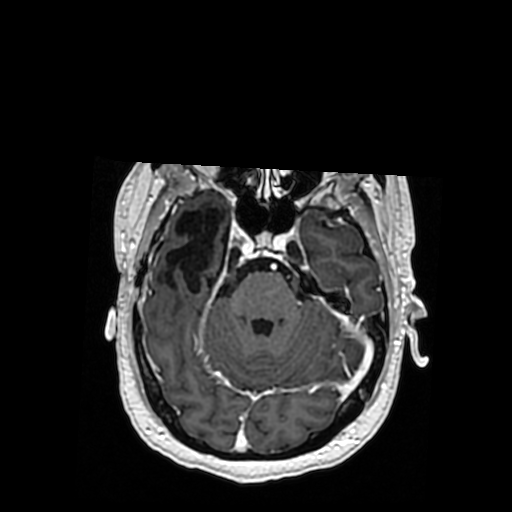
Brain MRI from a brain-tumour surgery series, one axial slice; T1-weighted post-contrast; 512 × 512 image matrix. Case-level facts recorded for this patient, not image findings: histopathology: Oligodendroglioma; WHO grade: 3; IDH mutation: yes; tumour location: Right Posterior Temporal Inferior Parietal.
Outlined on this slice (manually delineated by an expert):
- previous resection cavity: bounding box [x1, y1, x2, y2] px = [161, 209, 228, 293]